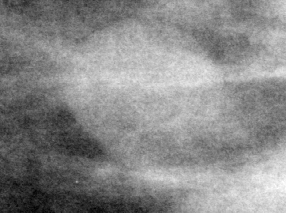
Cropped region of a digitized screen-film mammogram centred on a radiologist-marked abnormality, left breast, MLO view.
Mass, shape oval, margins circumscribed; BI-RADS assessment category 3; subtlety rating 5 on a 1 (subtle) to 5 (obvious) scale; pathology result (as recorded, not read from the image): benign.